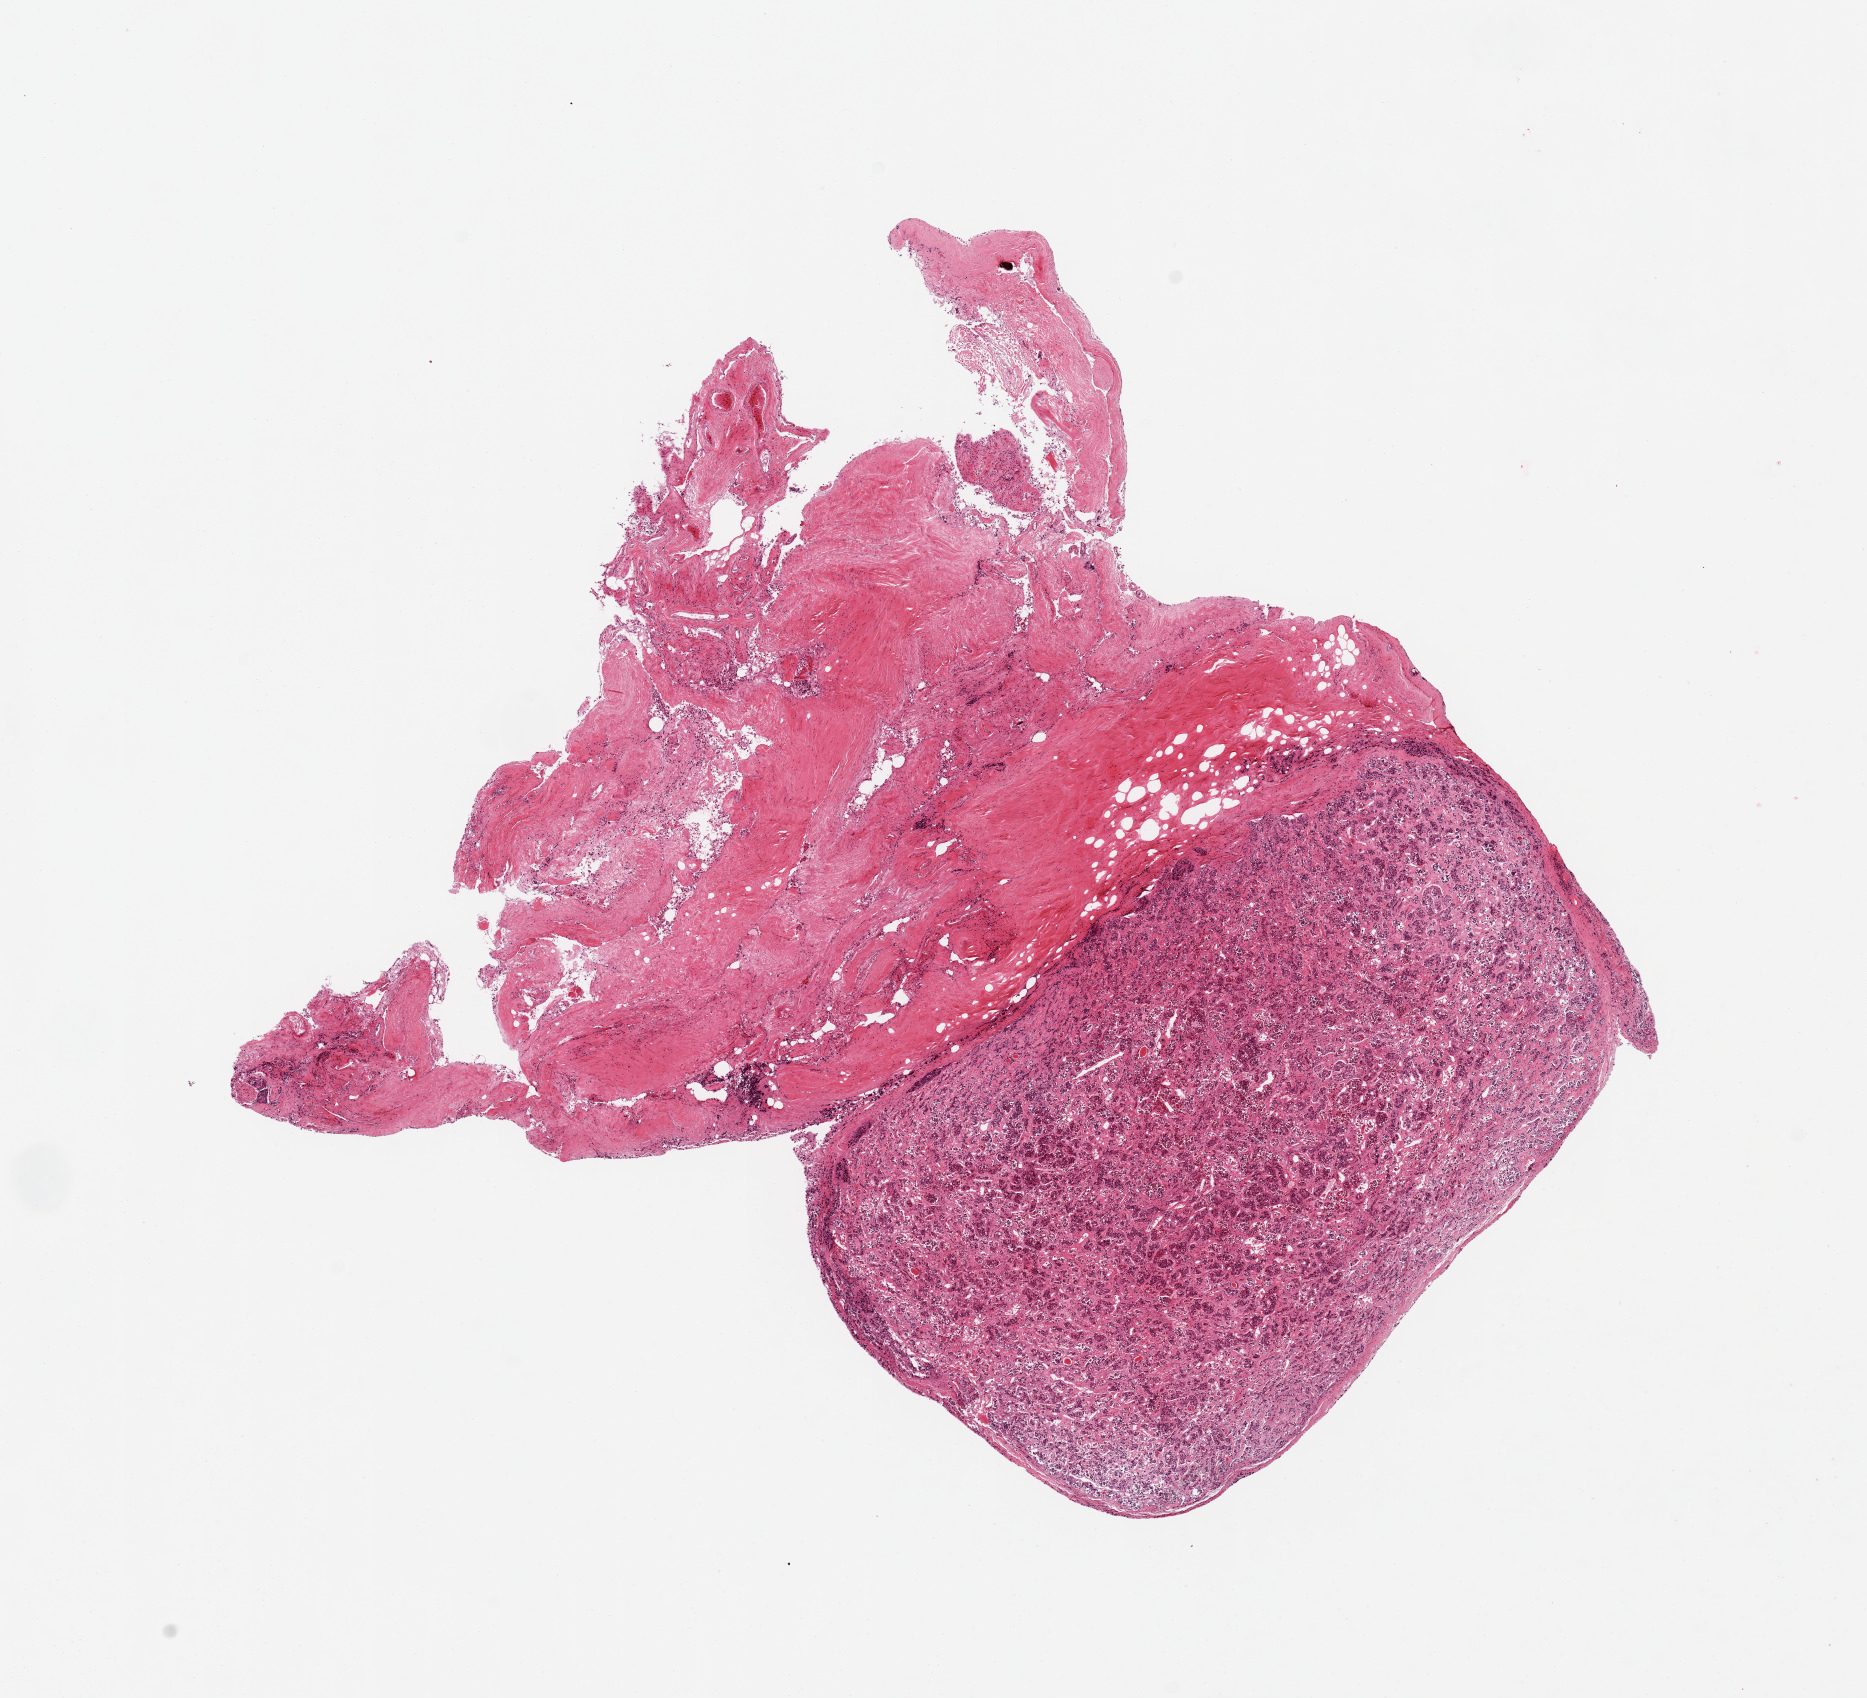
Hematoxylin and eosin (H&E) whole-slide image, shown as a low-resolution overview of the whole scanned area (about 14.8 x 13.4 mm, slide scanned at 20x); PAXgene-fixed, paraffin-embedded tissue; target tissue: pituitary; tissue donor sample. Male donor.
Review note (as recorded): 1 pieces; adenohypophysis and dura, small fragment of neurohypophysis.